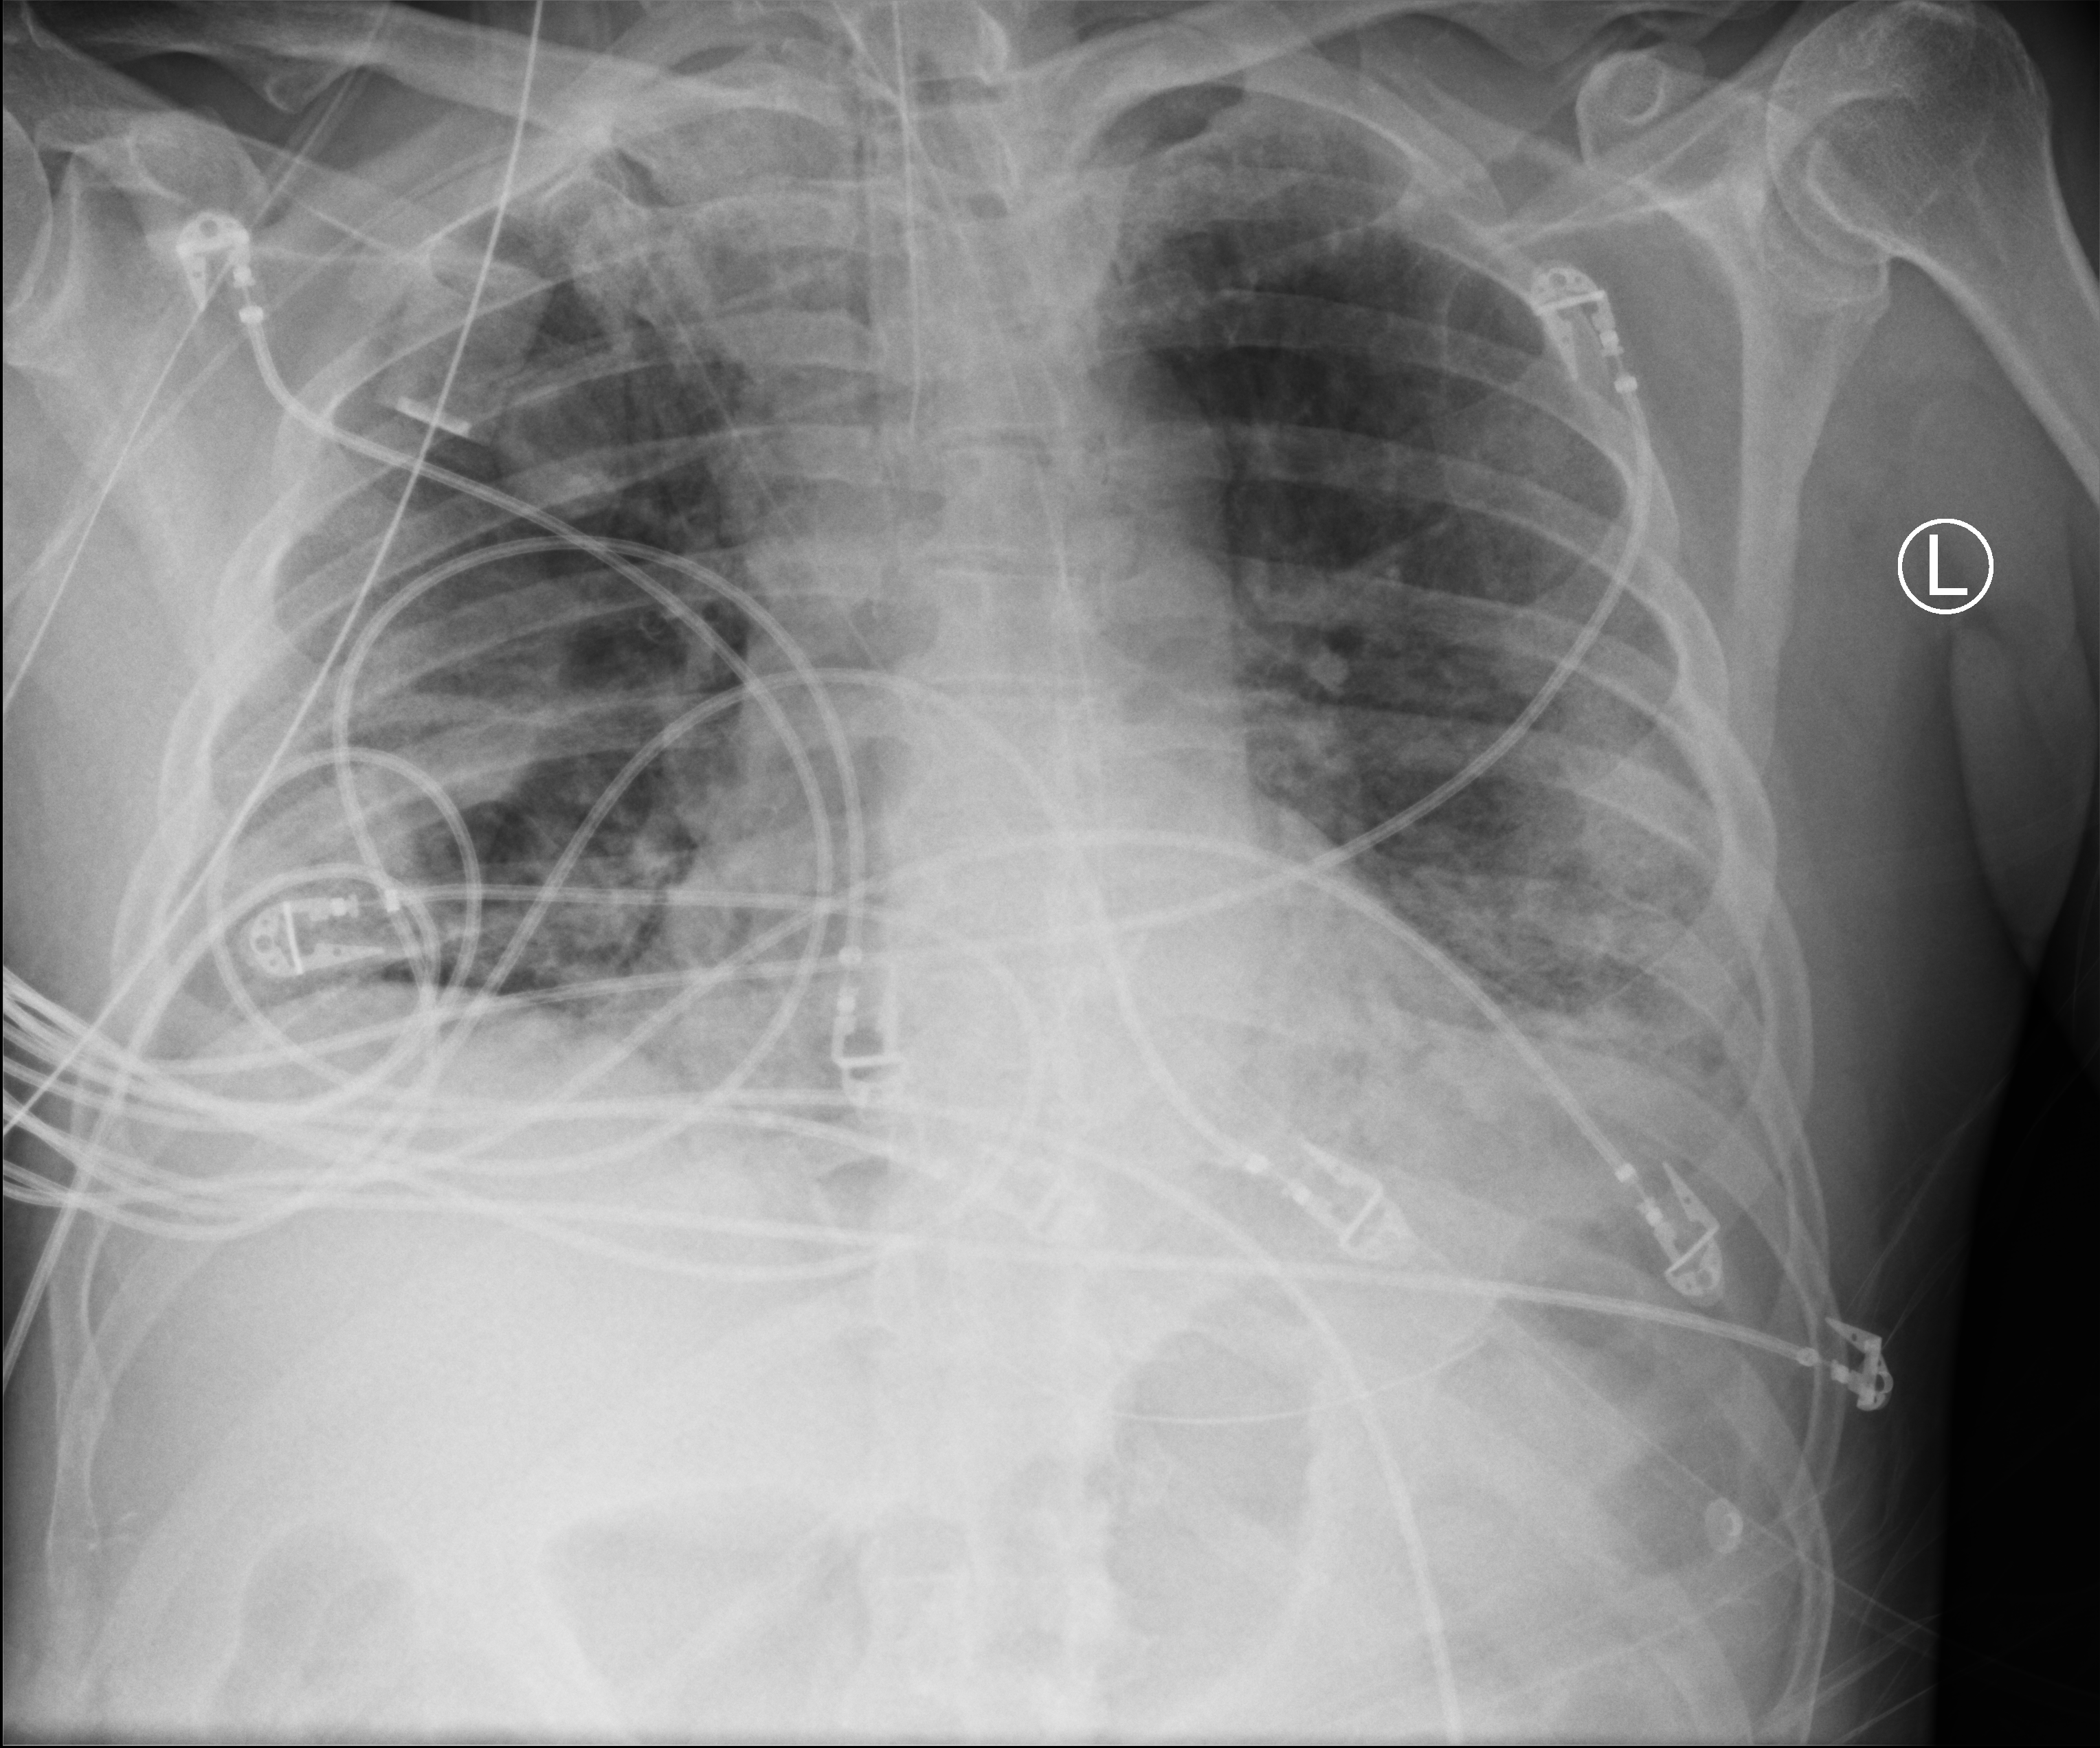
Chest X-ray (portable). Male patient hospitalised with COVID-19, age 60–74 years.
Admission-level facts for this patient (not findings on this image; timing relative to this image not recorded): admitted to intensive care during this hospital stay: yes.